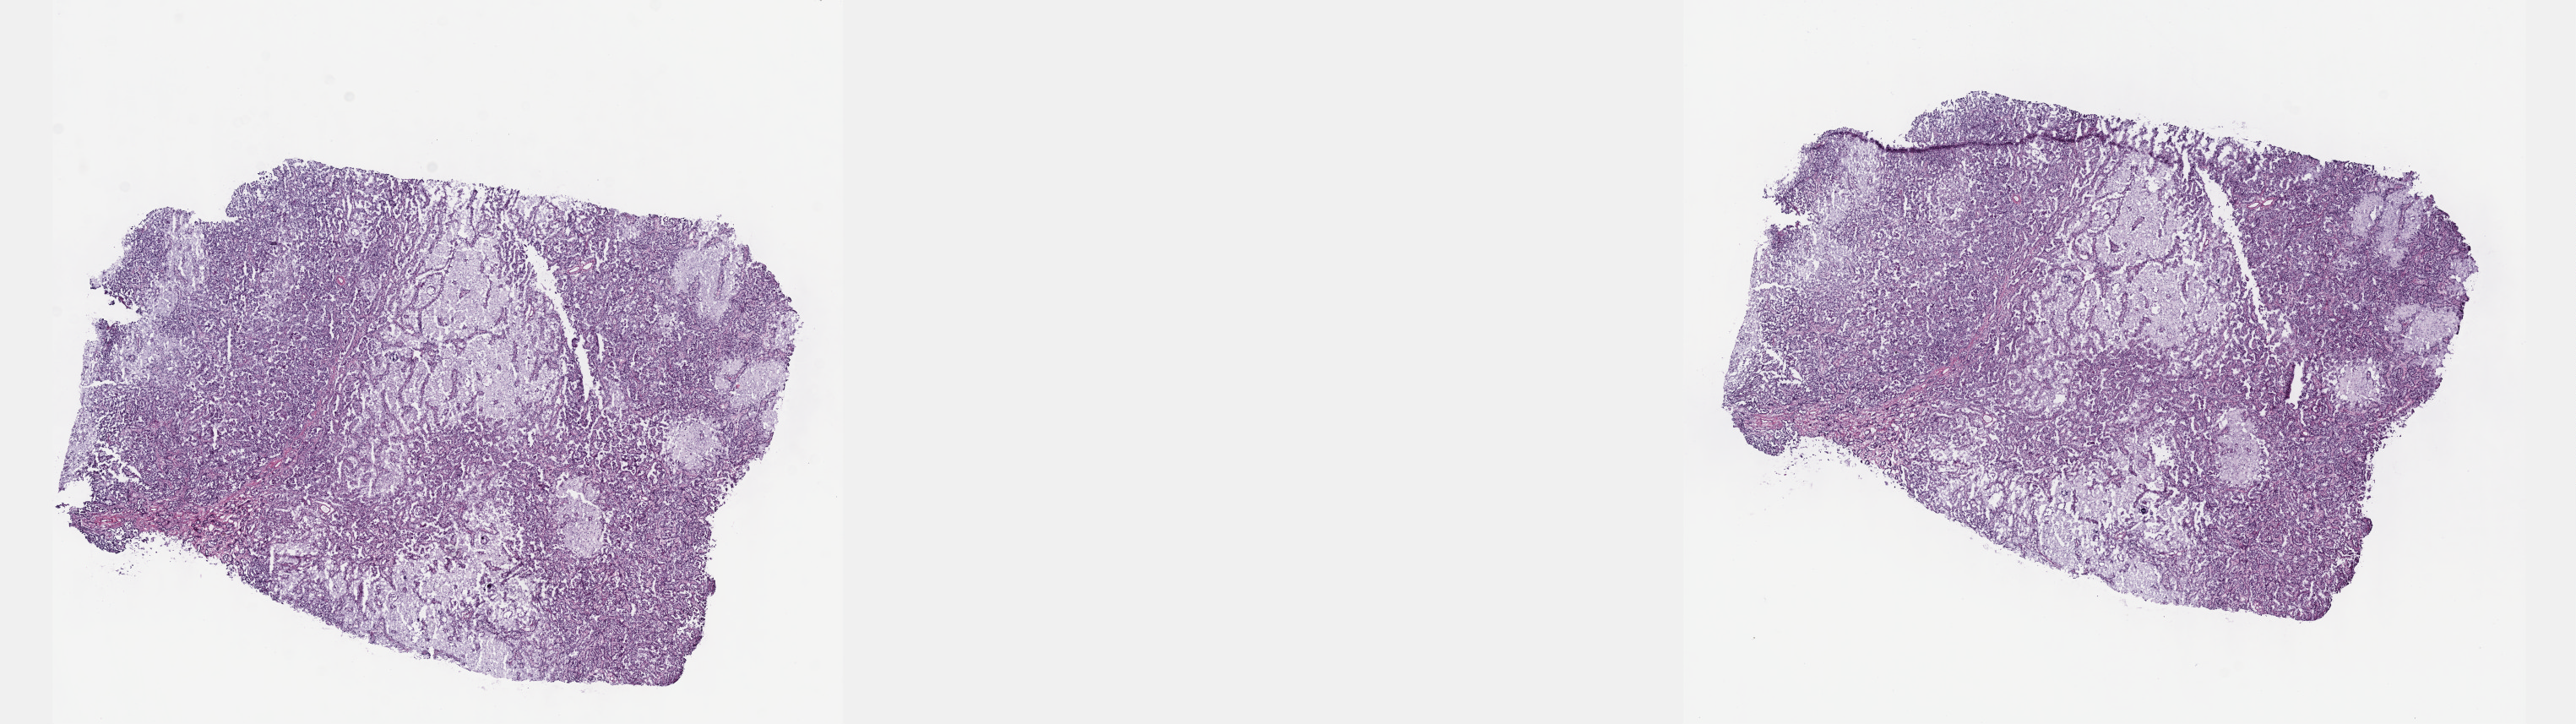
H&E whole-slide image, low-resolution overview of the scanned area, about 24.6 x 6.9 mm (from a 40x scan). Frozen section from the top of the tissue portion. Primary tumour sample from the kidney. Patient: male, age at initial diagnosis 28 years. Pathologist review of this section (percent, as recorded): tumour cells 70%, tumour nuclei 70%, normal cells 0%, stromal cells 30%, necrosis 0%. Inflammatory infiltration, as recorded: lymphocyte infiltration 0%, monocyte infiltration 15%, neutrophil infiltration 0%.
Laterality: left. AJCC pathologic stage: I. TNM: T1a NX MX. Pathologic diagnosis: Papillary adenocarcinoma, NOS.